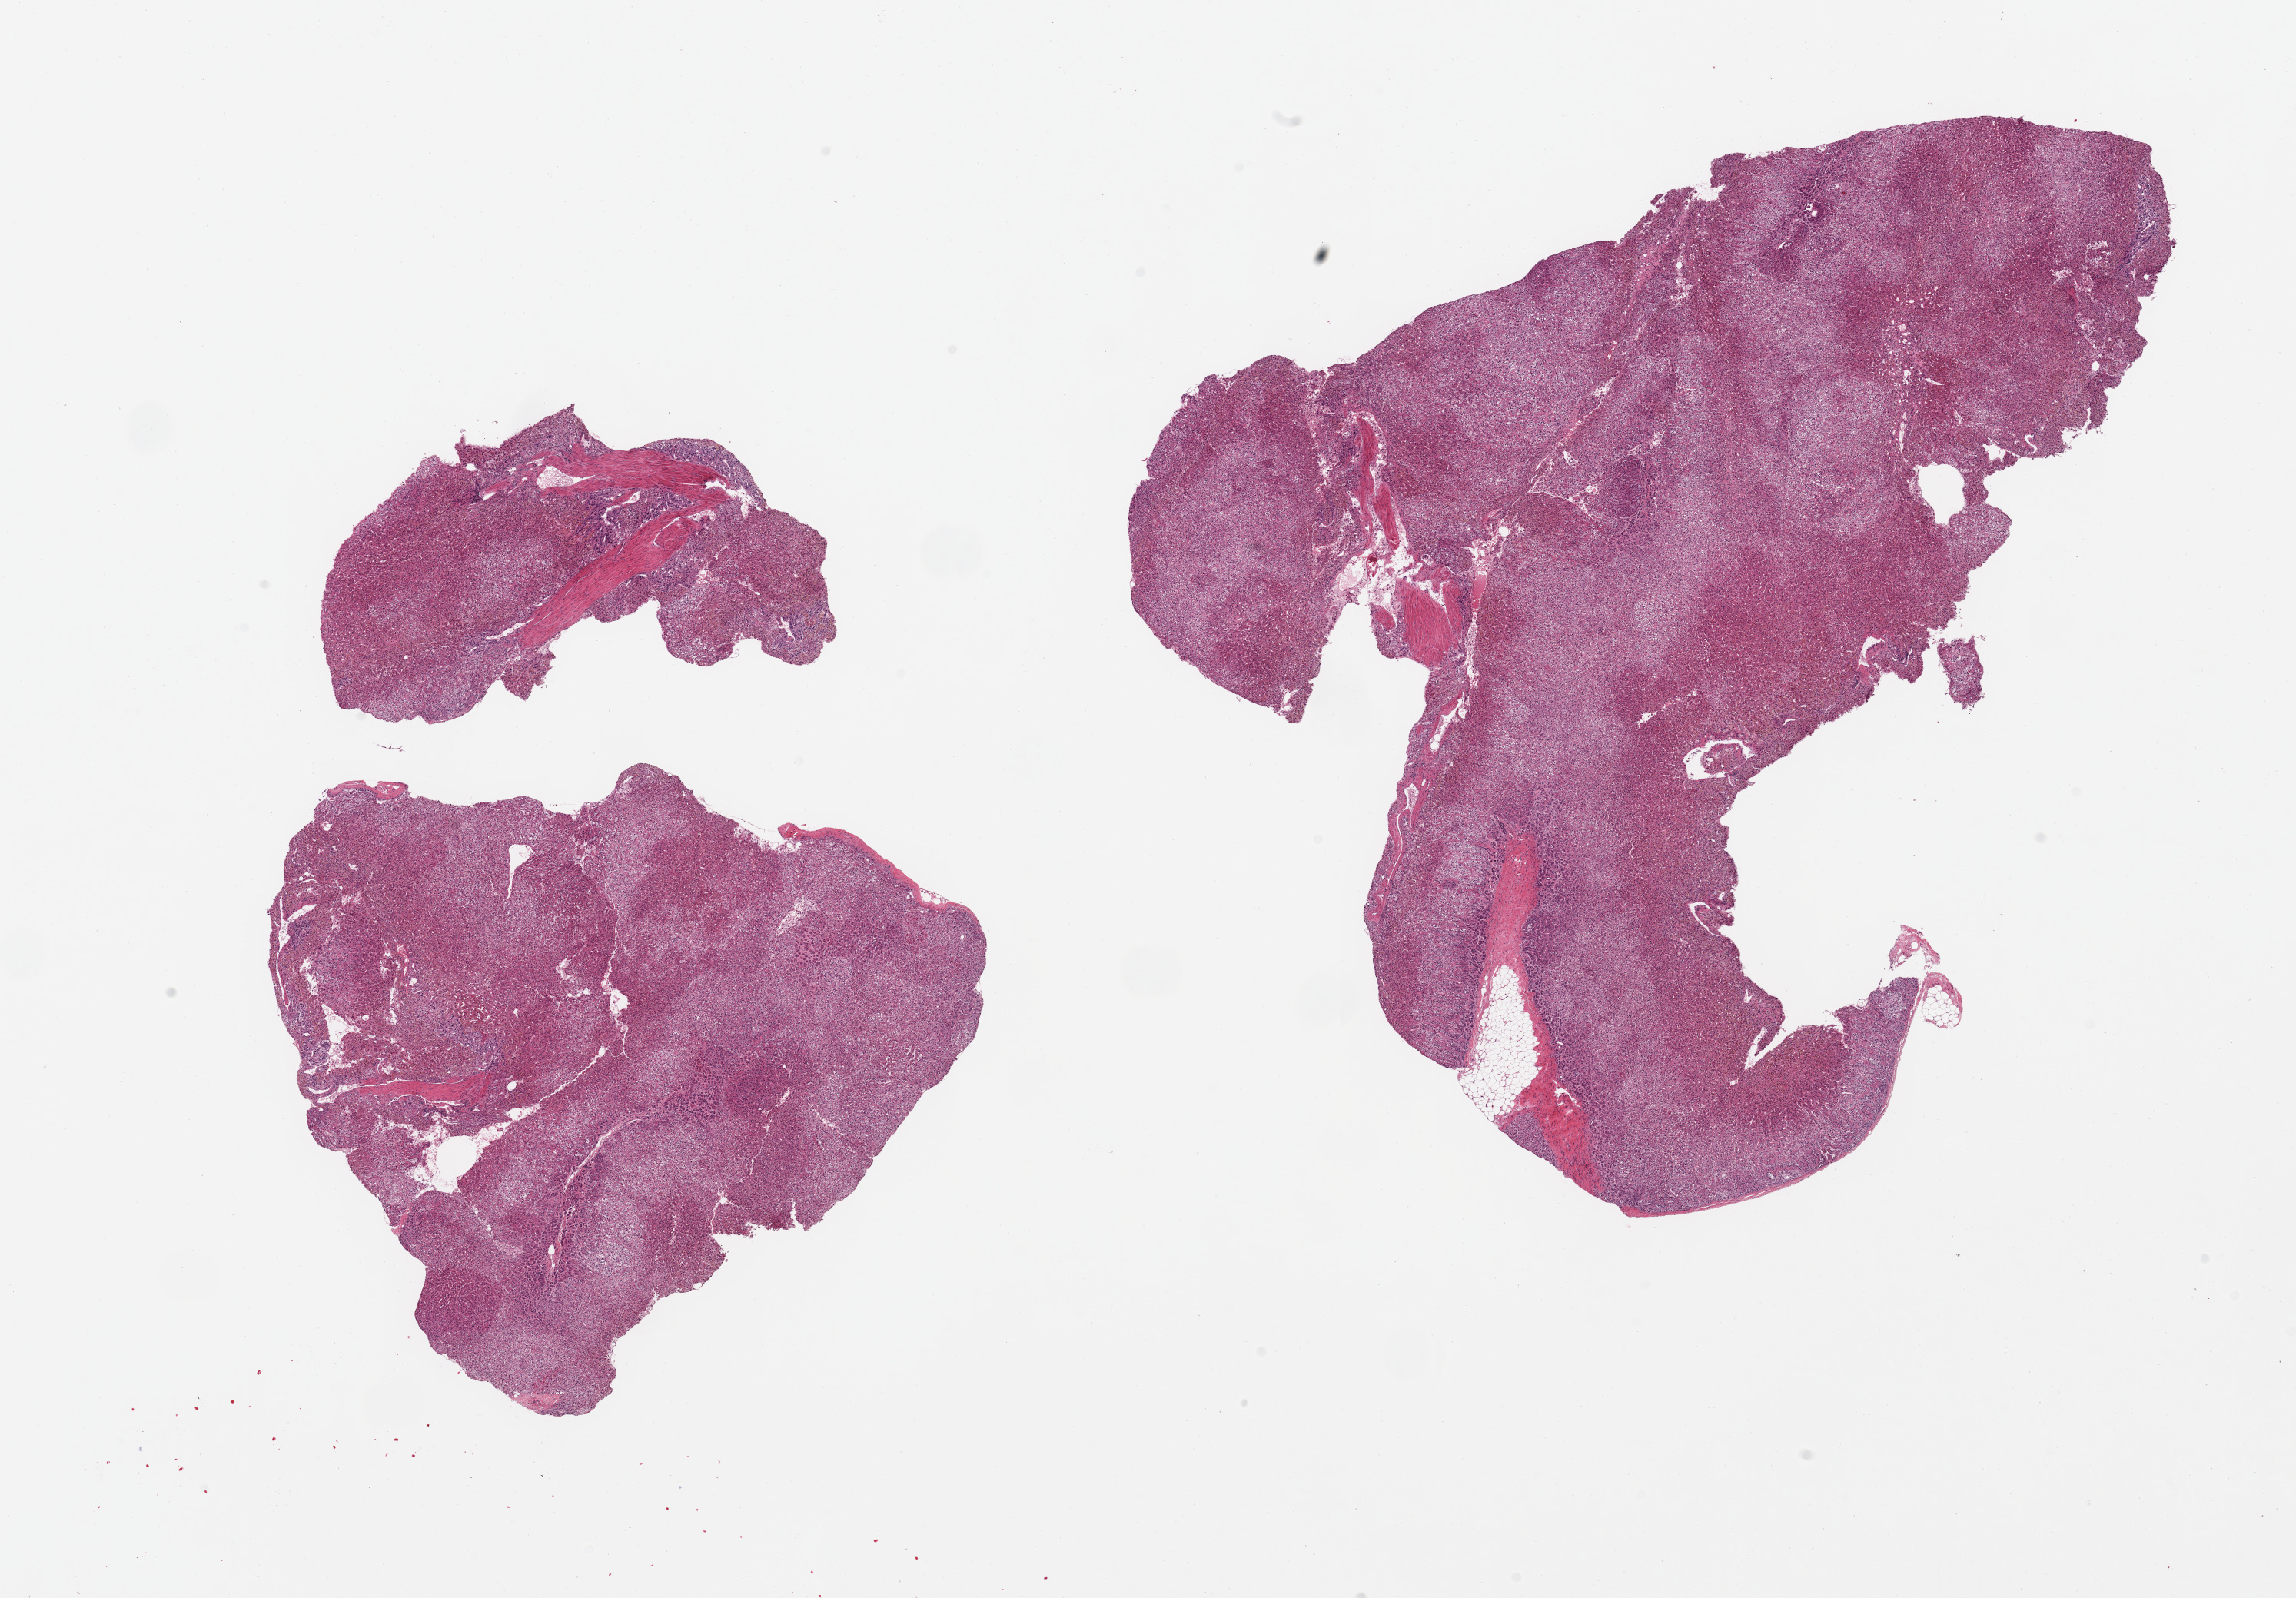
Haematoxylin and eosin whole-slide image, a low-resolution overview of the entire scanned area, about 23.6 x 16.4 mm, PAXgene-fixed paraffin-embedded (PFPE) section, sampled site (target tissue): adrenal gland, tissue donor sample. Donor sex: male.
Reviewer comment on this tissue sample: 2 pieces, all cortex.